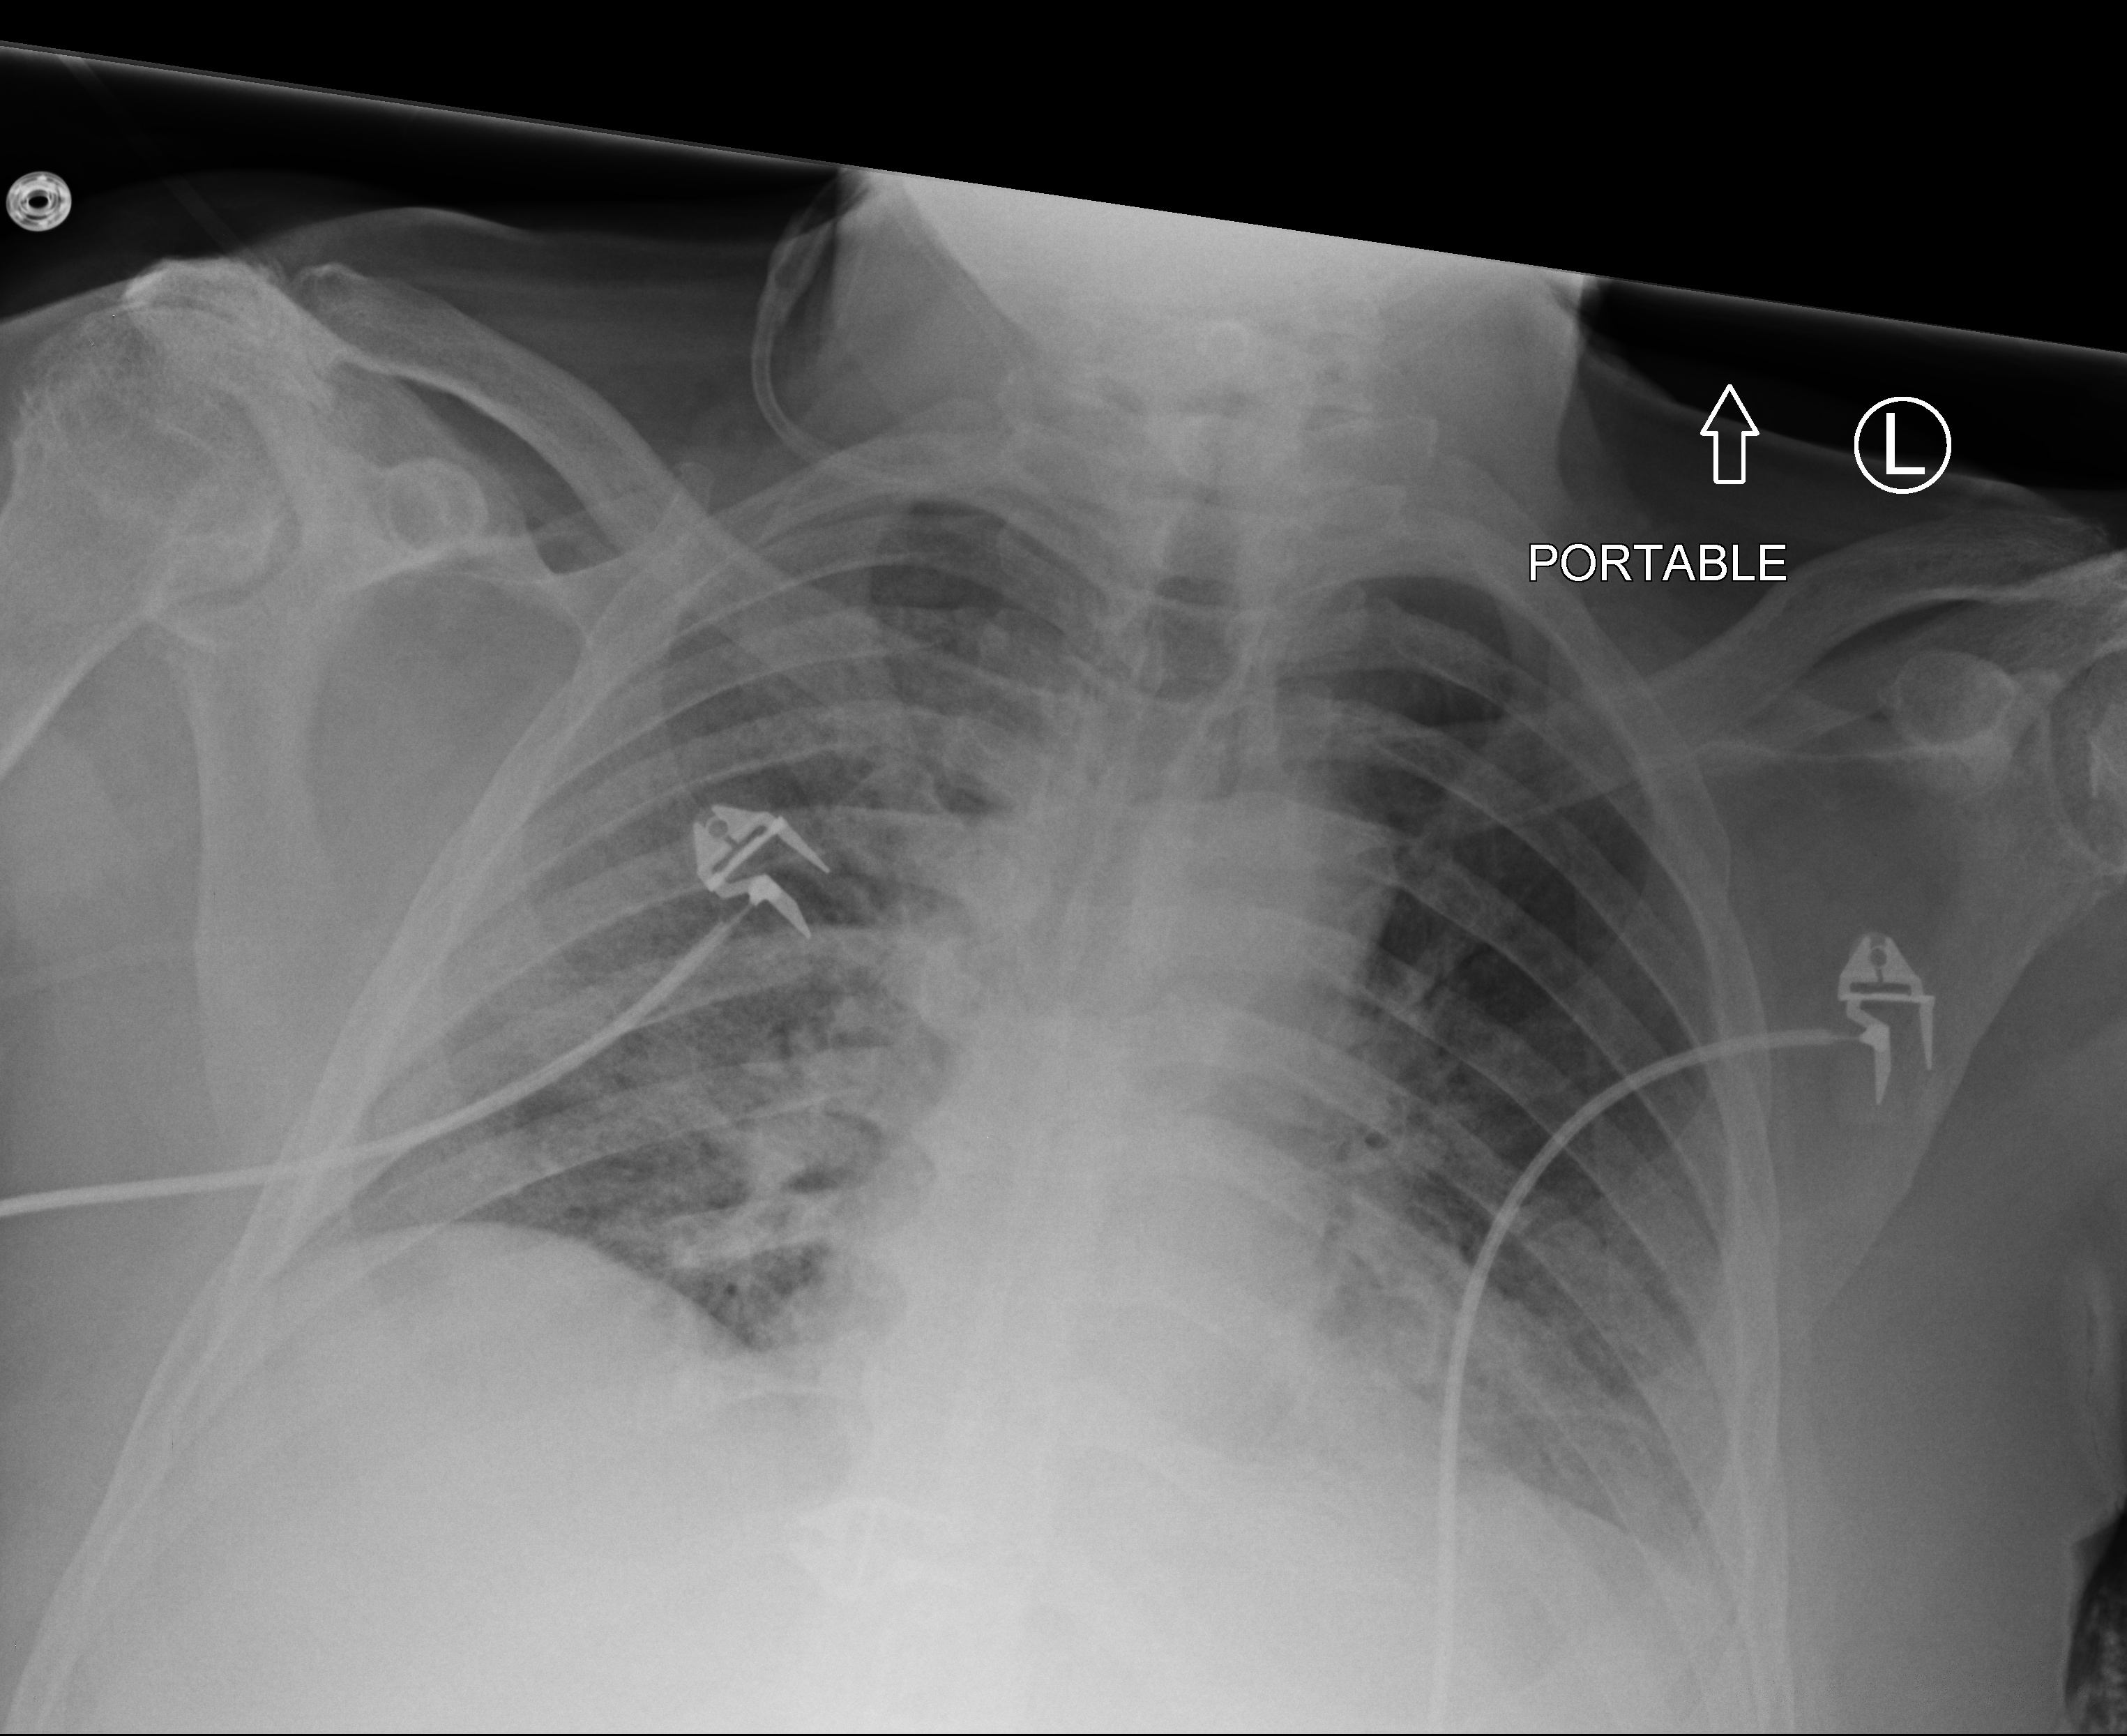
Bedside chest radiograph (computed radiography), anteroposterior (AP) projection. Male patient hospitalised with COVID-19, age 75–90 years.
Hospital-stay facts (about this admission, not read from this image; timing relative to this image not recorded): diabetes (admission record): no; length of hospital stay: 12 days; COPD (admission record): no.